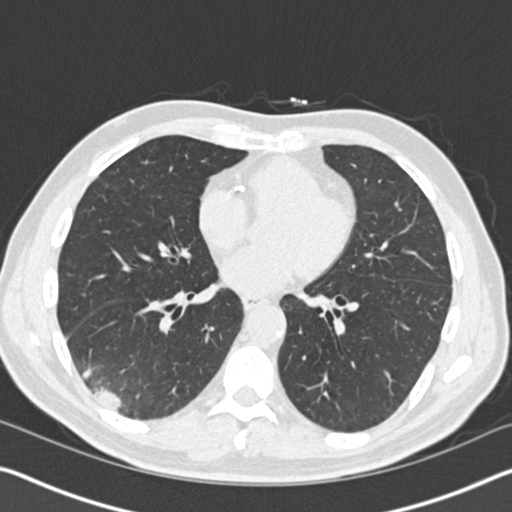
Chest CT (low-dose screening protocol), one axial image. Baseline screening round. Lung window (W 1500 / L -600 HU). Standard (soft-tissue) reconstruction kernel (B30f). 512 × 512 image matrix. Male participant, aged 61 years at enrolment. Current smoker at enrolment.
Lesion marked by an expert reader, box from (x=53, y=334) to (x=162, y=426) px. Reader record for this screening exam (exam-level; its link to the box is not recorded): non-calcified nodule or mass ≥4 mm, right lower lobe, 52 × 36 mm, spiculated (stellate) margins, soft tissue attenuation. Official screen result: positive, change unspecified: nodule(s) >= 4 mm or enlarging nodule(s), mass(es), or other non-specific abnormalities suspicious for lung cancer. Participant outcome: lung cancer diagnosed 392 days after this screen (after the second annual screen) — bronchiolo-alveolar adenocarcinoma, NOS, right lower lobe, moderately differentiated (G2), stage IIIB (AJCC 6th edition), 90 mm at pathology.